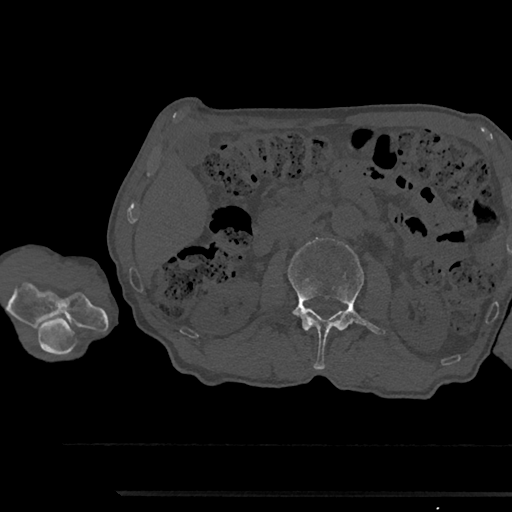
CT including the spine, one axial slice. Slice 563 of 797 in the series (ordered by position). 120 kVp. Bone window (W 1800 / L 400 HU). 0.5 mm slice thickness. 512 × 512 image matrix, field of view 367 × 367 mm. Male patient, age 79 years. From the clinical record (not read from this slice): primary cancer: prostate.
Annotated regions visible in this slice (semi-automatically segmented with operator editing):
- L2 vertebra: bounding box [x1, y1, x2, y2] px = [287, 237, 384, 369]